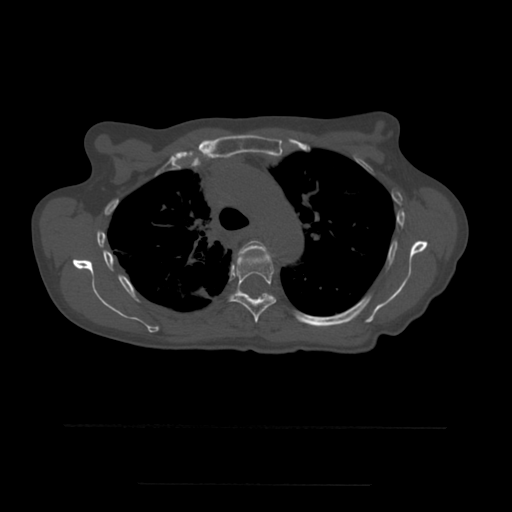
CT including the spine, one axial slice. Position 393 of 544 along the scan axis. Bone window (W 1800 / L 400 HU). 1.25 mm slice thickness. 512 × 512 image matrix, field of view 350 × 350 mm. Patient age 58 years. Case-level facts recorded for this patient, not image findings: primary cancer: lung.
Outlined on this slice (semi-automatically segmented with operator editing):
- T4 vertebra: bounding box [x1, y1, x2, y2] px = [237, 241, 269, 259]
- T5 vertebra: [229, 252, 277, 323]
- T6 vertebra: [262, 294, 268, 296]